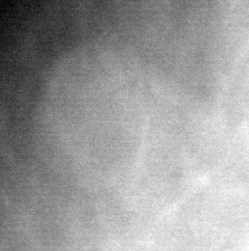
Cropped region of a digitized screen-film mammogram centred on a radiologist-marked abnormality, right breast, CC view, BI-RADS breast density category 1 (scale 1–4).
Marked abnormality: mass, shape round, margins circumscribed; BI-RADS assessment category 2; pathology result (as recorded, not read from the image): benign.